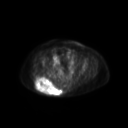
FDG PET of an extremity soft-tissue mass (from a PET/CT study), one axial slice; 3.27 mm slice thickness; 128 × 128 image matrix, field of view 600 × 600 mm. Patient: female, 60 years. From the clinical record (not read from this slice): histological type: spindle cell suggestive of myxofibrosarcoma; grade: intermediate; site of the primary tumour: right buttock.
Structures marked on this image (expert contour drawn on MRI and transferred to this co-registered scan by the dataset authors):
- gross tumour volume (mass): bounding box (x1, y1, x2, y2) in pixels: (35, 77, 62, 96)